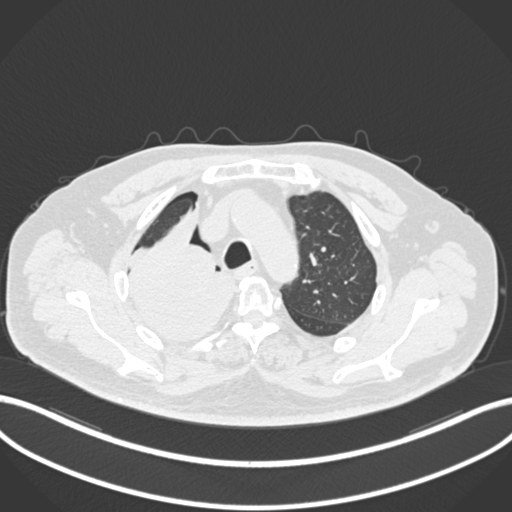
Chest CT, one axial slice; position 164 of 218 along the scan axis; lung window (W 1500 / L -600 HU); 1 mm slice thickness; 512 × 512 image matrix. Patient: male, 68 years. From the clinical record (not read from this slice): clinical TNM (as recorded): T2a N0 M0.
Outlined on this slice (rectangle marked by the reading radiologist):
- lung tumour (recorded histology: adenocarcinoma): bounding box <136,204,228,341> (left, top, right, bottom; pixels)